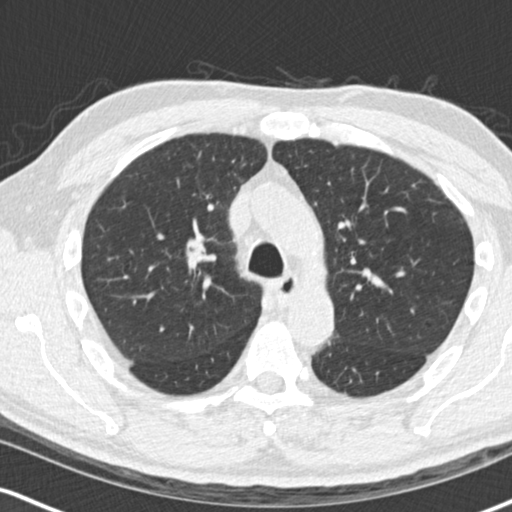
Low-dose screening chest CT, one axial slice. Slice 108 of 170 in the series (ordered by position). Reconstruction kernel B30f. Lung window (W 1500 / L -600 HU). 2 mm slice thickness. 512 × 512 image matrix, field of view 320 × 320 mm.
Annotated regions visible in this slice (expert manual segmentation):
- lesion 1 (tumor, upper lobe of right lung): box from (x=186, y=239) to (x=209, y=261) px